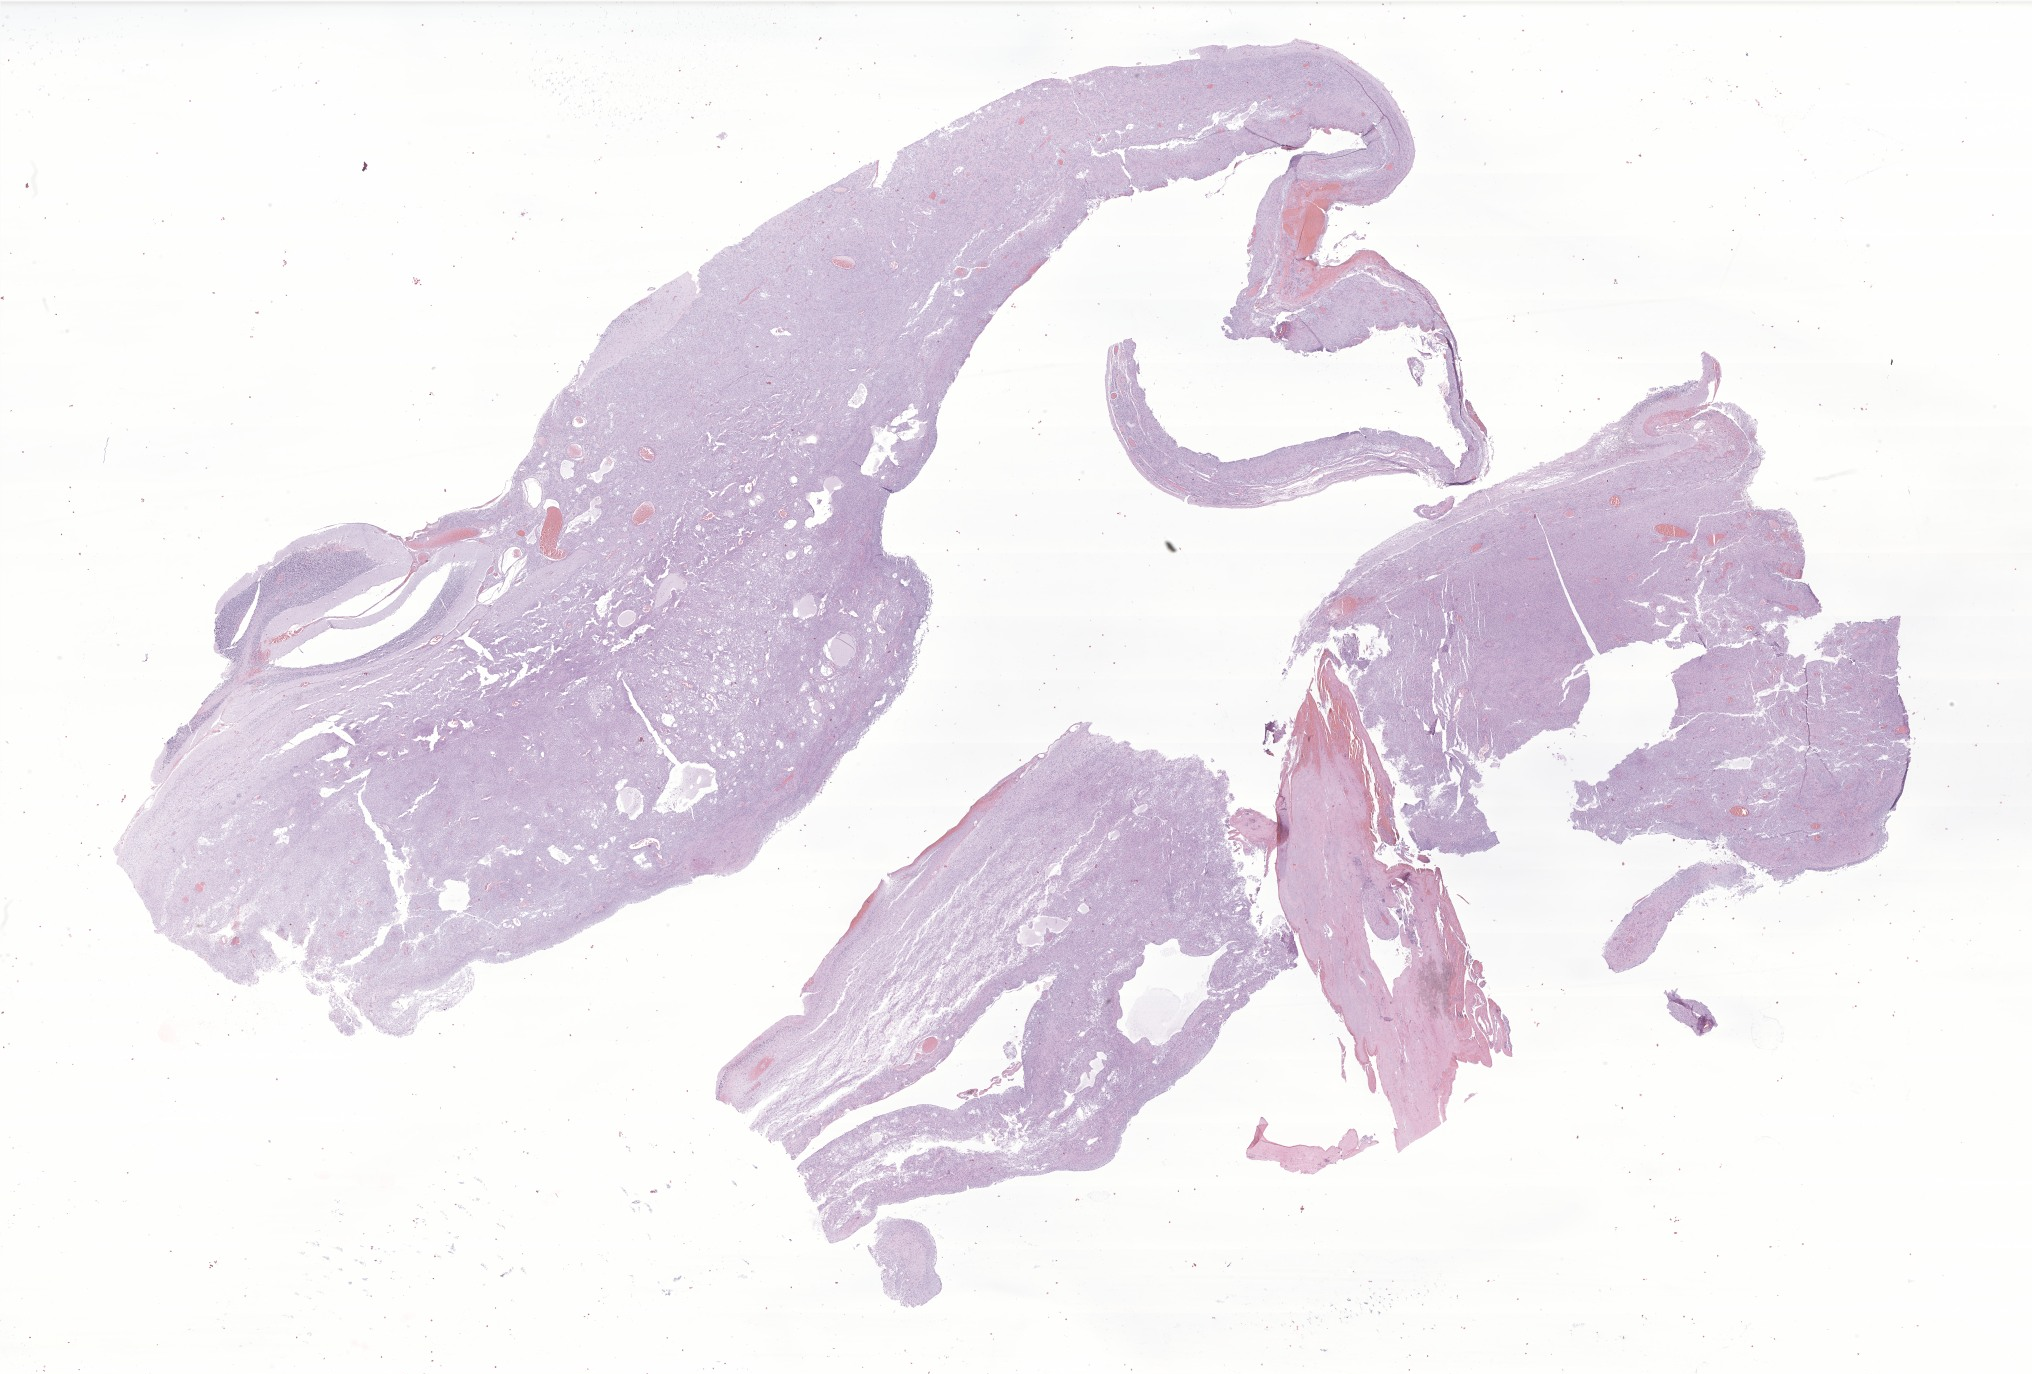
Haematoxylin and eosin whole-slide image of tumor tissue from the cerebellum — shown as a low-resolution overview of the whole scanned area (about 34.3 x 23.2 mm), formalin-fixed, paraffin-embedded (FFPE) tissue. Male patient, age 40 months (3 years 4 months).
* diagnosis: Pilocytic astrocytoma